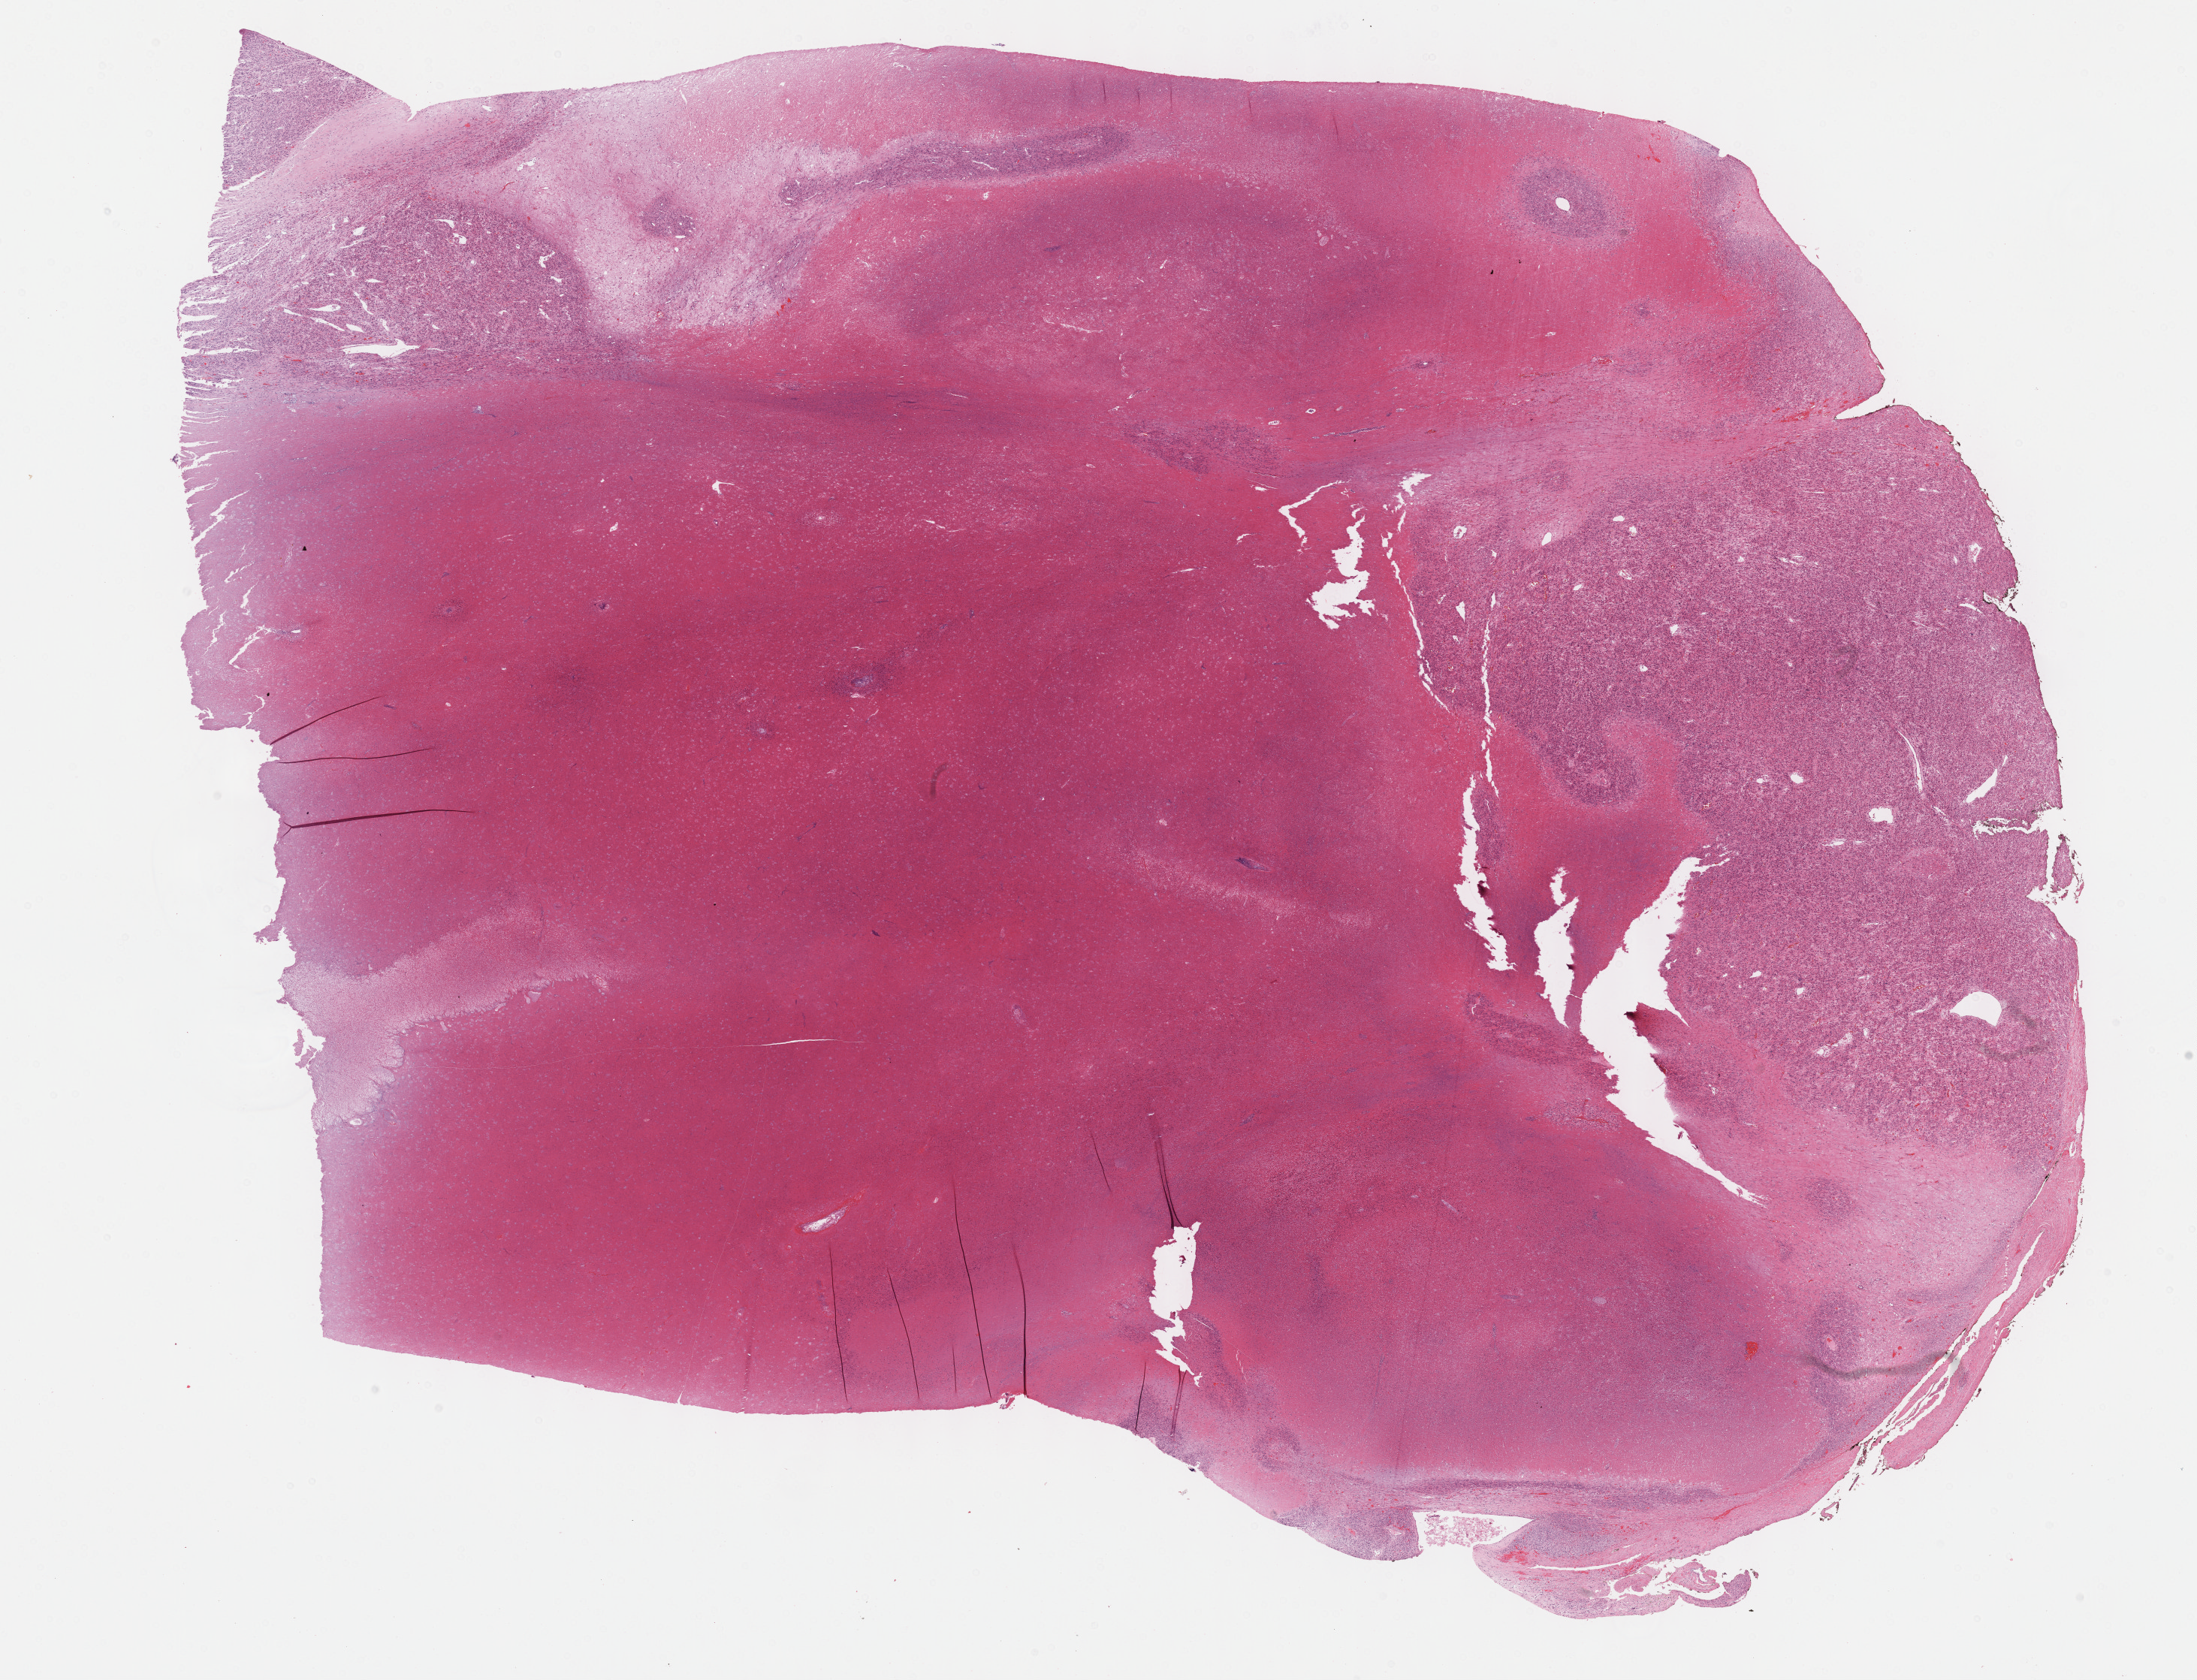
H&E whole-slide image, low-resolution overview of the scanned area, about 23.7 x 18.1 mm, formalin-fixed paraffin-embedded (FFPE) diagnostic section, sample: primary tumour, retroperitoneum and peritoneum. Female, age 53 years at initial diagnosis.
Pathologic diagnosis: Leiomyosarcoma, NOS (retroperitoneum).